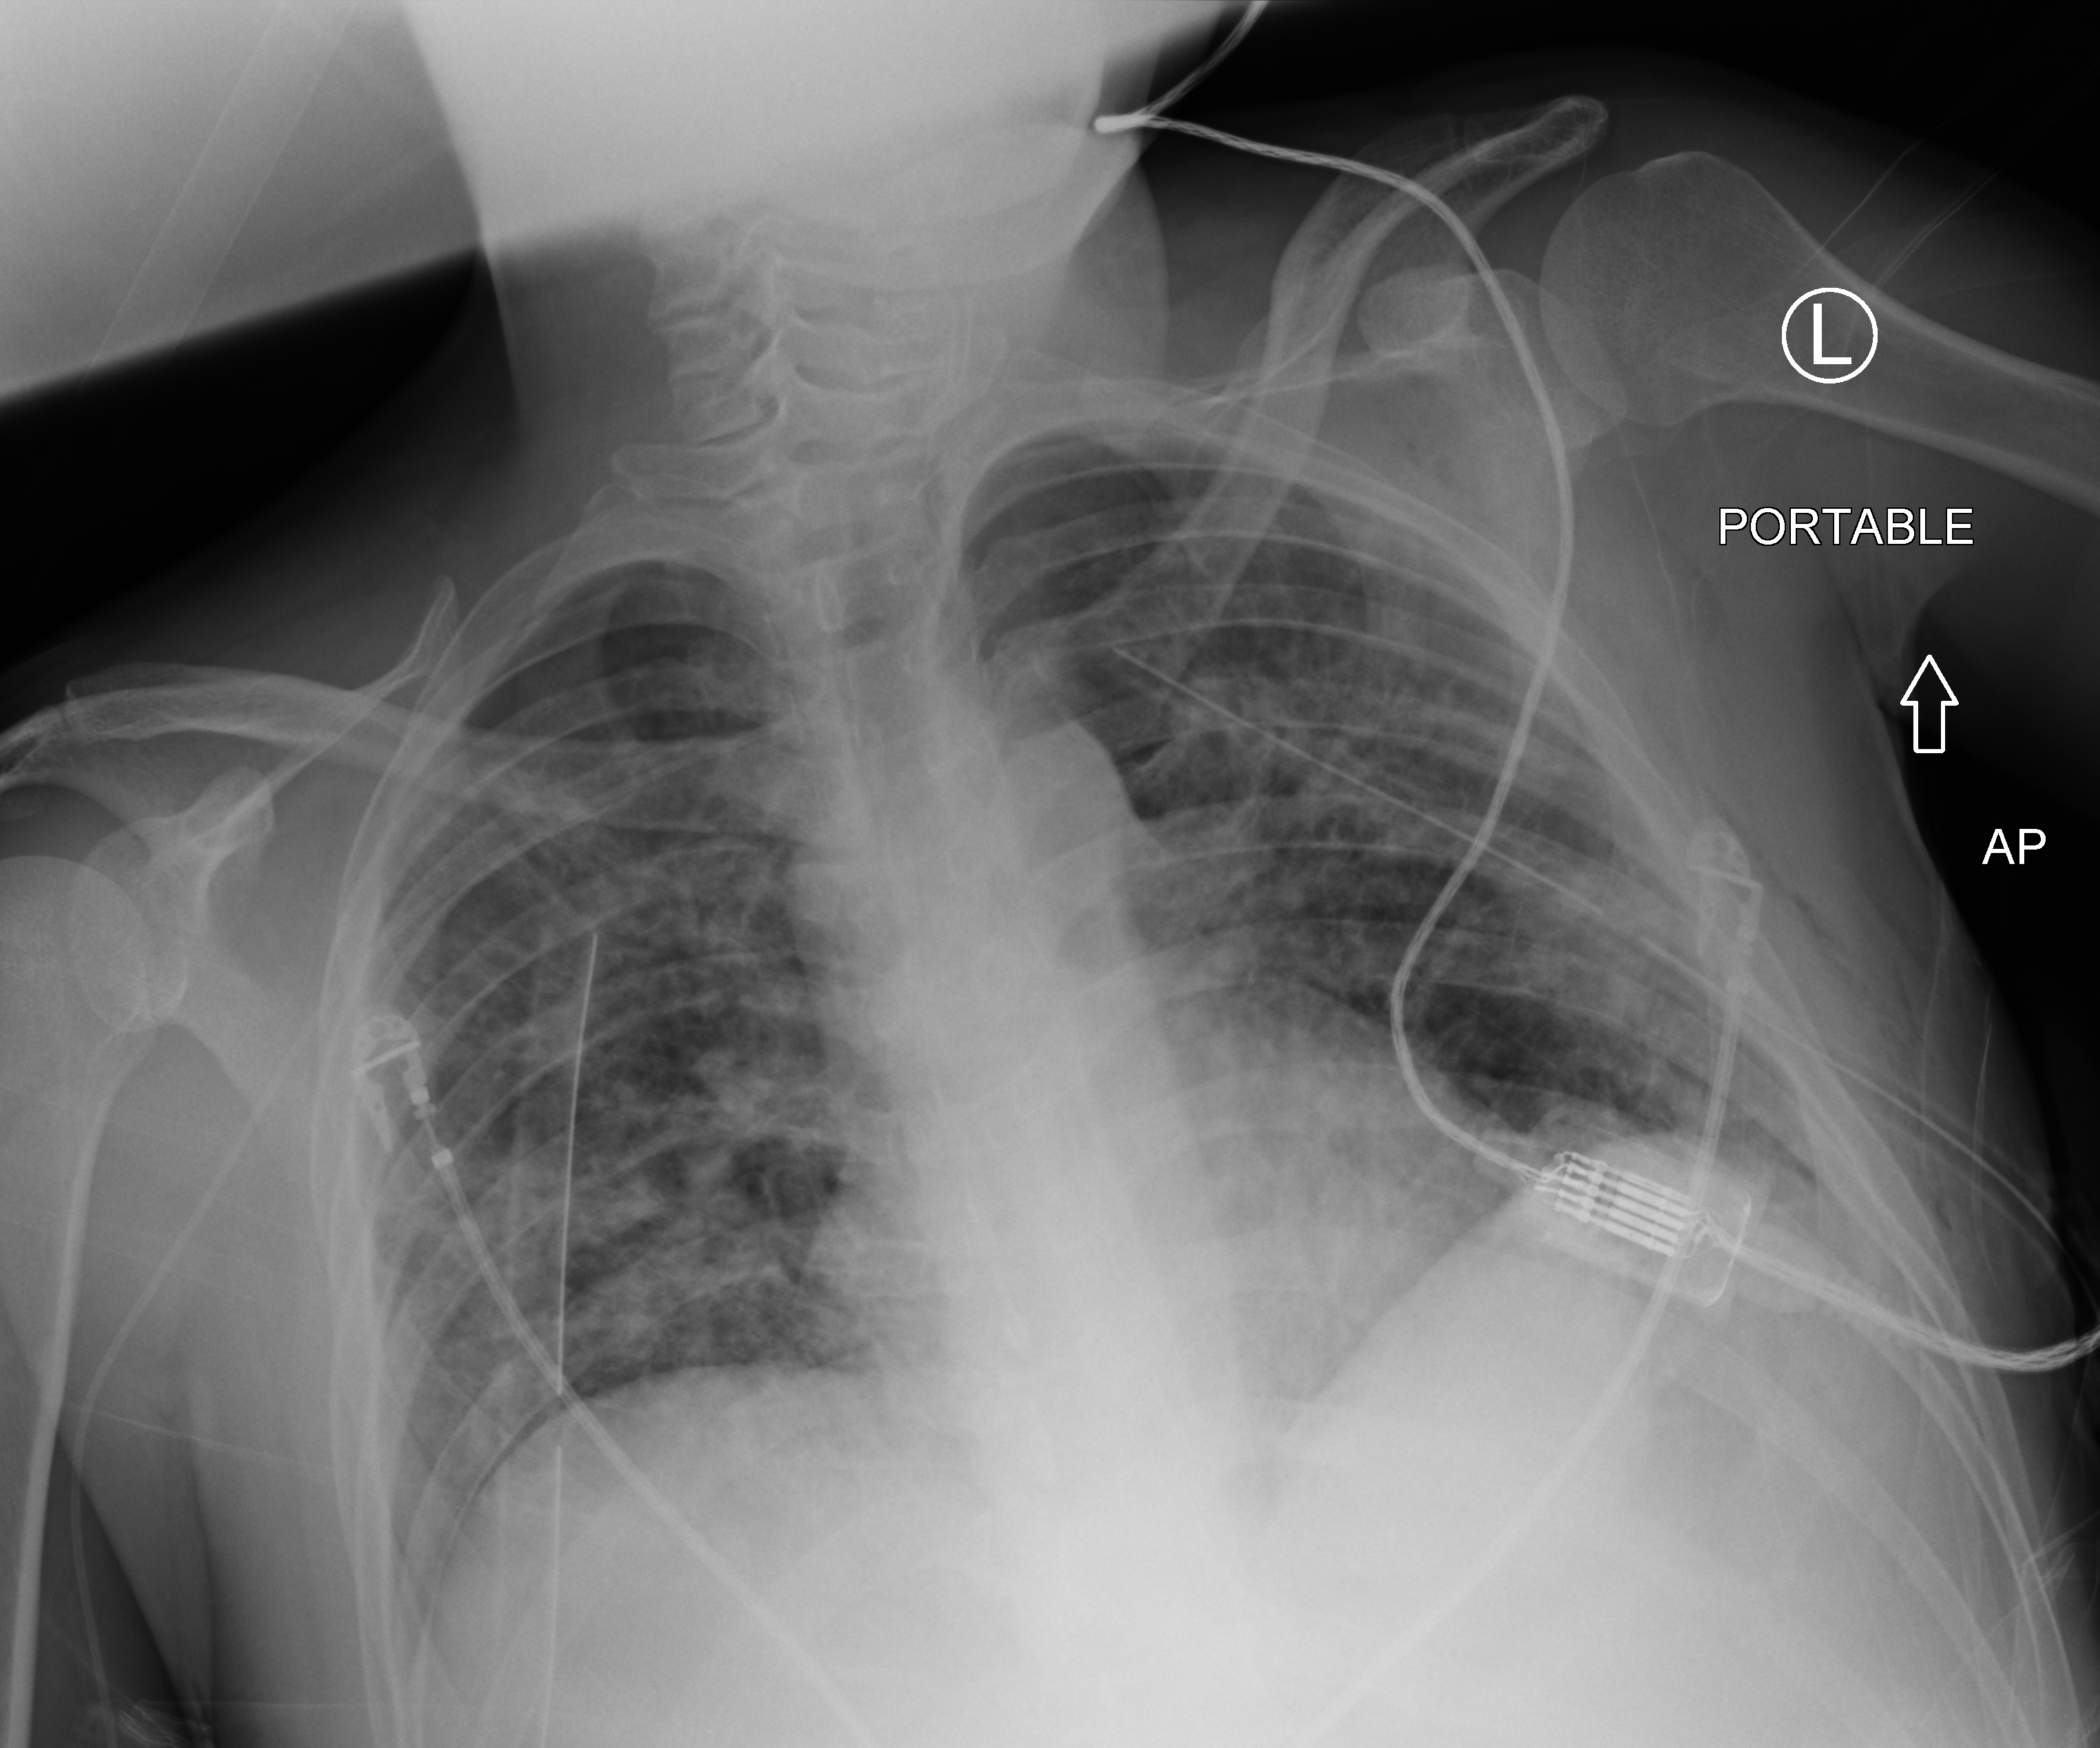
Chest X-ray (portable), anteroposterior (AP) projection. Male patient hospitalised with COVID-19, age 18–59 years.
Admission-level facts for this patient (not findings on this image; timing relative to this image not recorded): mechanically ventilated during this hospital stay: yes; COPD (admission record): no.